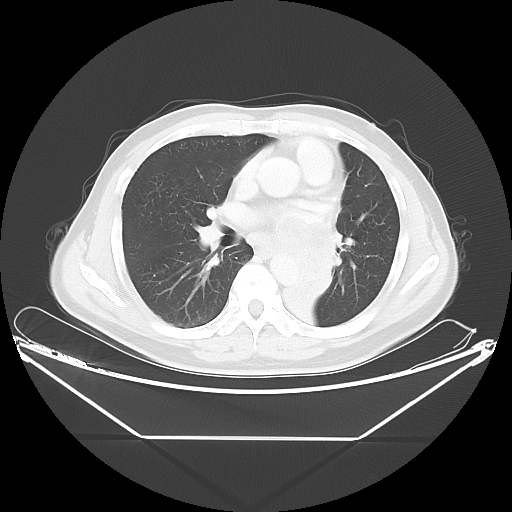
Chest CT, one axial slice; slice 24 of 48 in the series (ordered by position); reconstruction kernel LUNG; lung window (W 1500 / L -600 HU); 512 × 512 image matrix, field of view 438 × 438 mm. Male patient, age 58 years. Case-level facts recorded for this patient, not image findings: clinical TNM (as recorded): T3 N3 M0.
Structures marked on this image (rectangle marked by the reading radiologist):
- lung tumour (recorded histology: squamous cell carcinoma): bounding box [x1, y1, x2, y2] px = [269, 215, 343, 329]